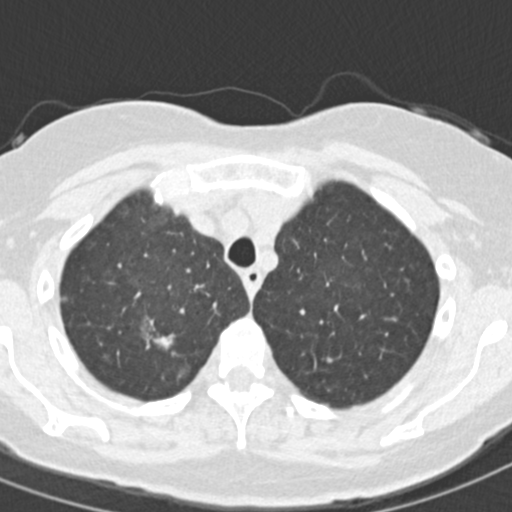
Low-dose screening chest CT, one axial slice. Position 125 of 157 along the scan axis. Reconstruction kernel B30f. 120 kVp. Lung window (W 1500 / L -600 HU). 2 mm slice thickness. 512 × 512 image matrix.
Structures marked on this image (outlined manually by an expert reader):
- lesion 1 (tumor, upper lobe of right lung): bounding box <145,333,176,352> (left, top, right, bottom; pixels)